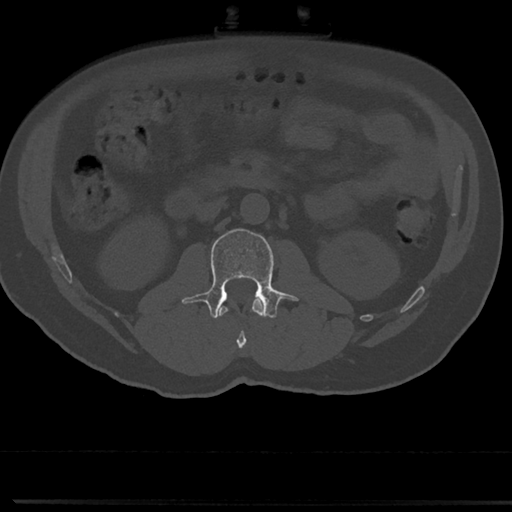
CT including the spine, one axial slice. Position 29 of 817 along the scan axis. Reconstruction kernel Br40s/3. Bone window (W 1800 / L 400 HU). 512 × 512 image matrix, field of view 355 × 355 mm. Male patient, age 61 years. From the clinical record (not read from this slice): primary cancer: prostate.
Outlined on this slice (semi-automatically segmented with operator editing):
- L1 vertebra: bounding box [x1, y1, x2, y2] px = [219, 298, 263, 351]
- L2 vertebra: [191, 228, 296, 319]